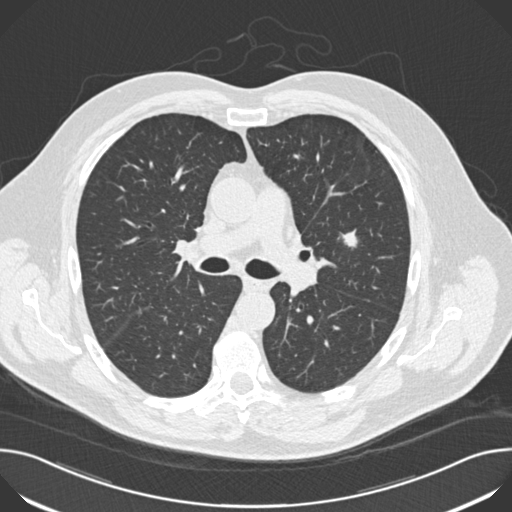
Low-dose screening chest CT, one axial slice. Position 107 of 174 along the scan axis. Reconstruction kernel B30f. Lung window (W 1500 / L -600 HU). 2 mm slice thickness. 512 × 512 image matrix, field of view 380 × 380 mm.
Annotated regions visible in this slice (manually delineated by an expert):
- lesion 1 (tumor, upper lobe of left lung): bounding box (x1, y1, x2, y2) in pixels: (338, 229, 357, 247)